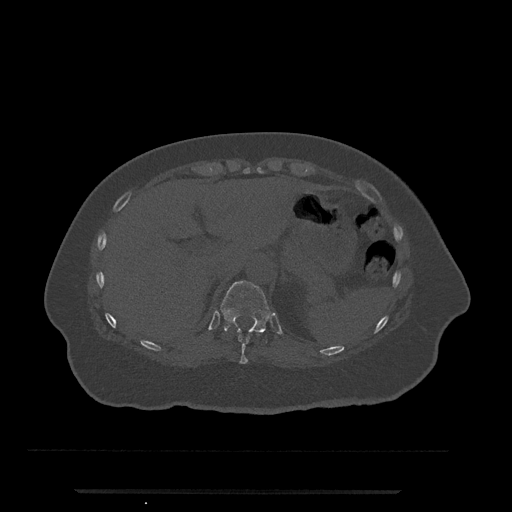
CT including the spine, one axial slice; position 249 of 797 along the scan axis; reconstruction kernel Br40s/3; bone window (W 1800 / L 400 HU); 512 × 512 image matrix. Female patient, age 51 years. Case-level facts recorded for this patient, not image findings: primary cancer: neuro.
Outlined on this slice (semi-automatically segmented with operator editing):
- T10 vertebra: bounding box [x1, y1, x2, y2] px = [238, 334, 259, 364]
- T11 vertebra: [221, 281, 271, 340]